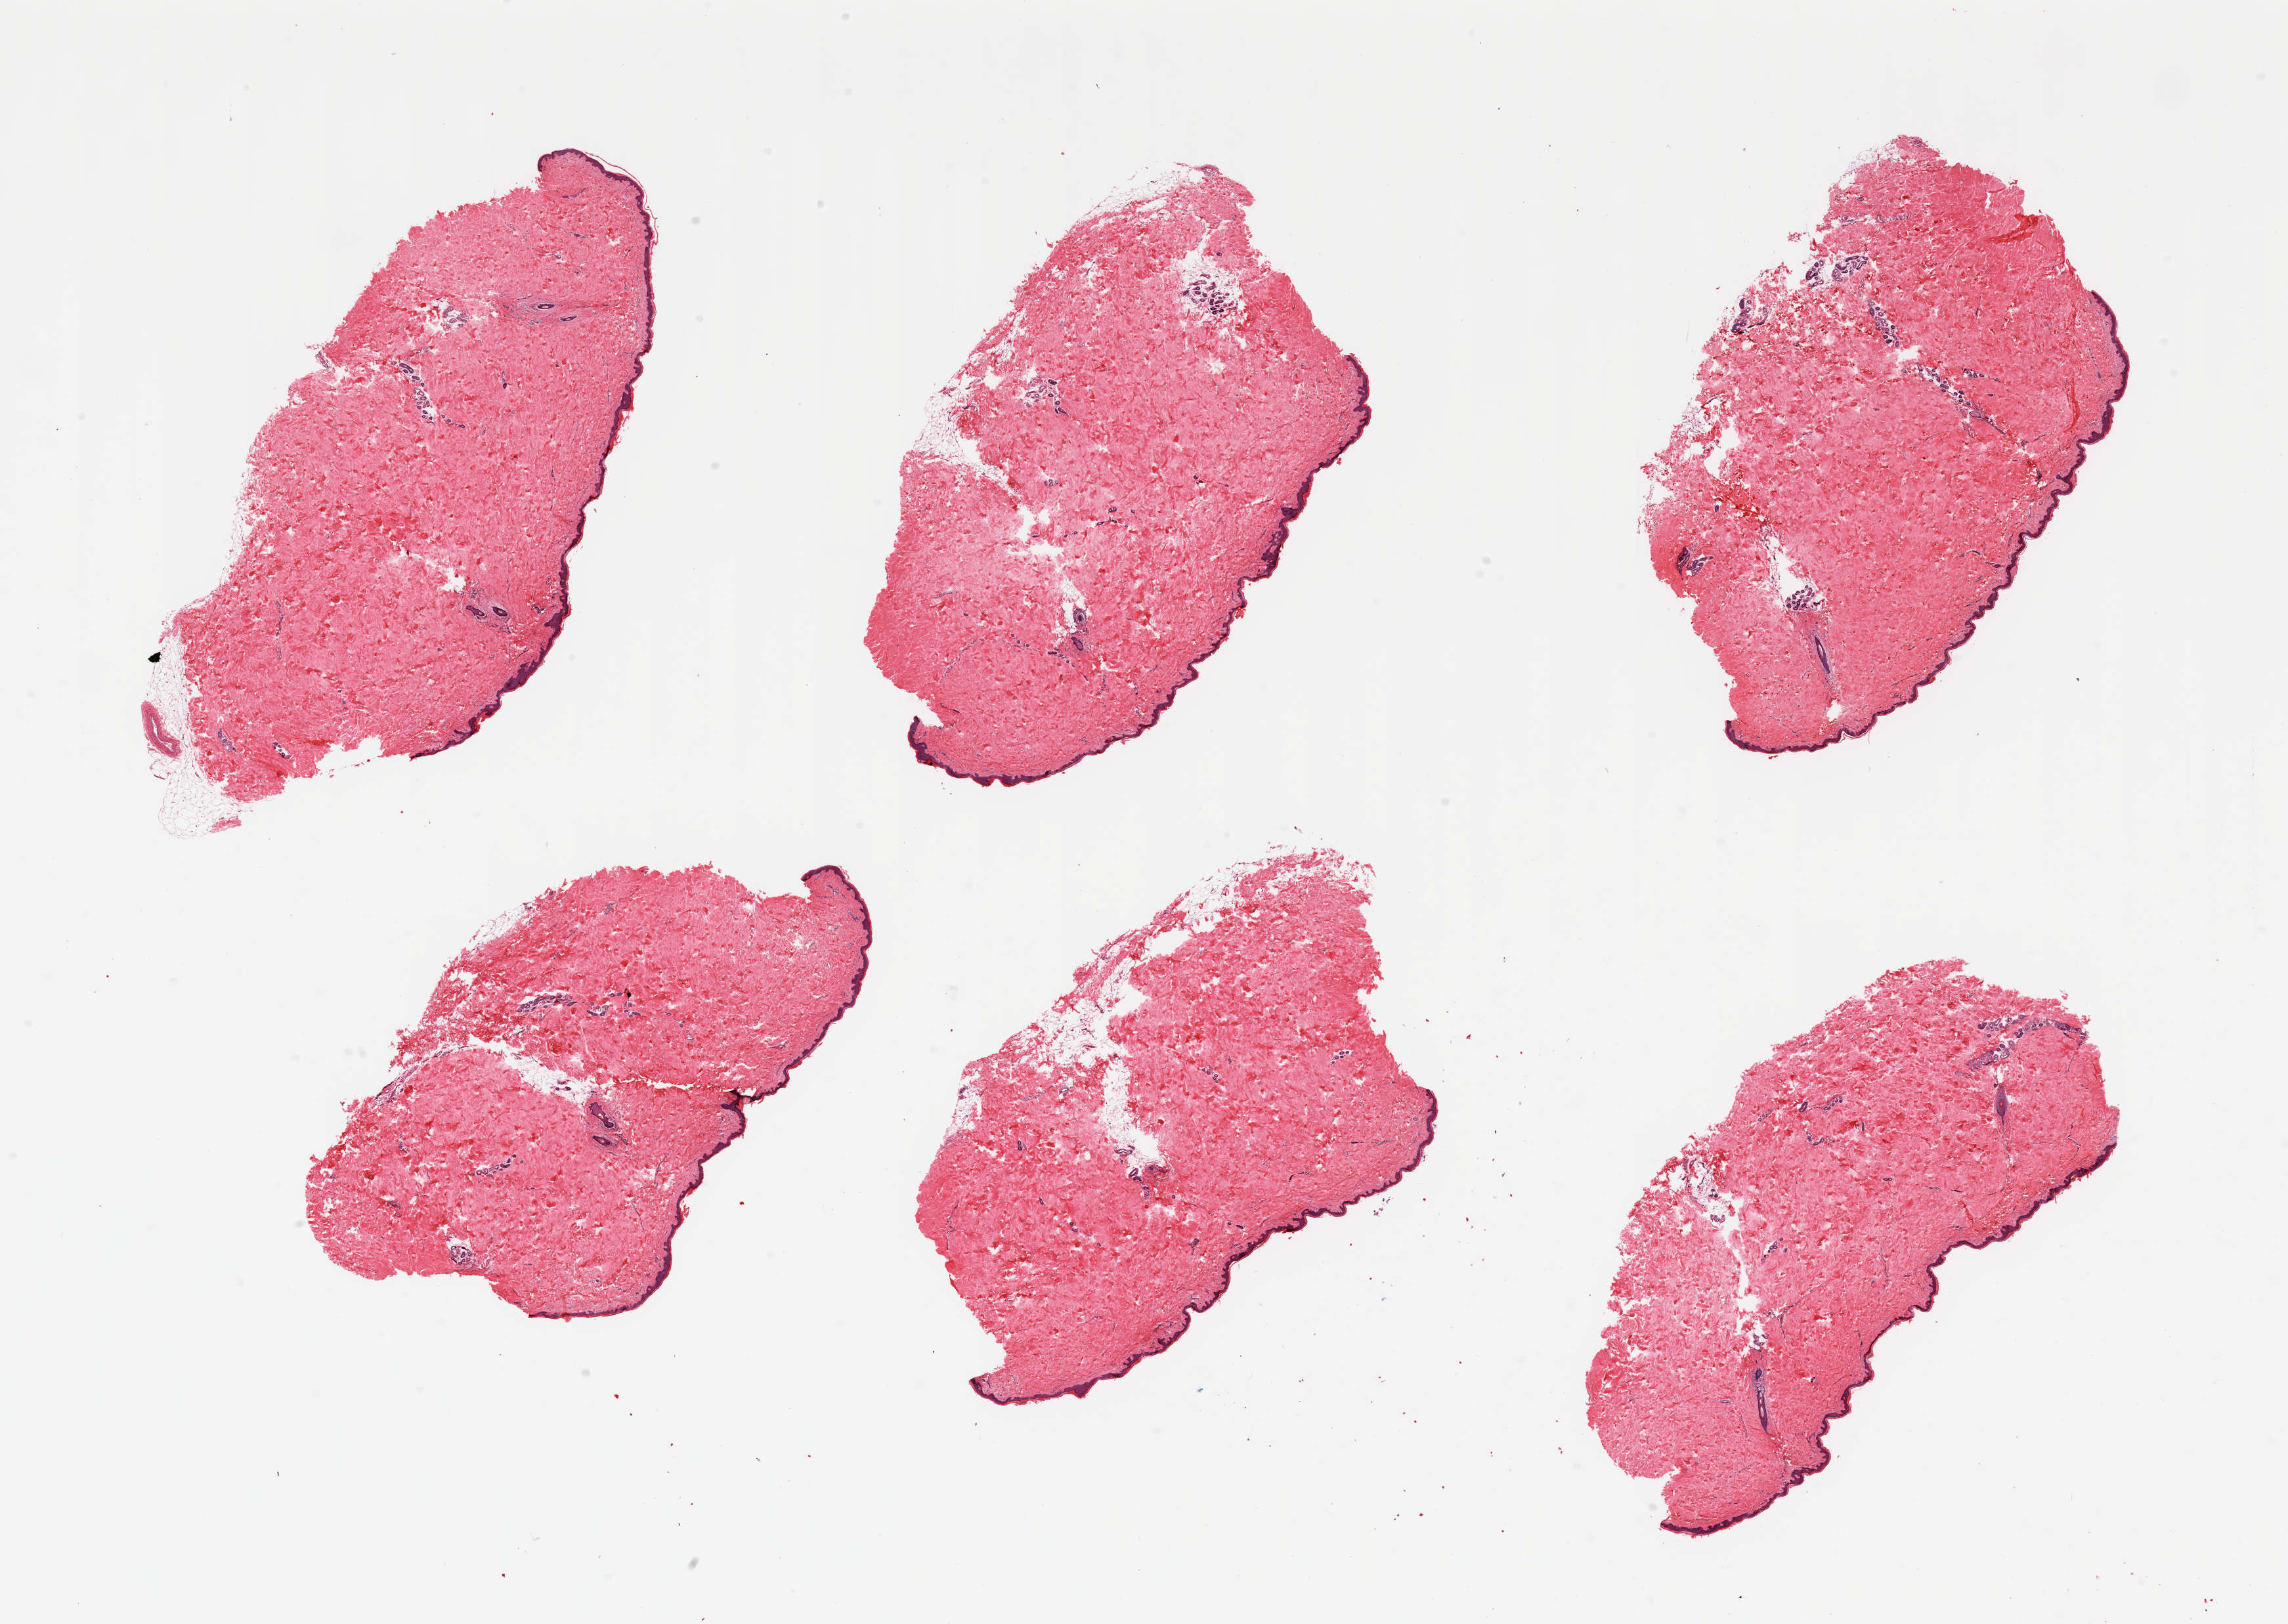
H&E whole-slide image, brightfield, whole scanned area (about 27.6 x 19.6 mm) shown as a low-resolution overview. PAXgene-fixed paraffin-embedded (PFPE) section. Section of skin of suprapubic region (target tissue). Donor tissue sample. Female donor.
Review note (as recorded): 6 pieces; predominantly well trimmed, minimal internal fat.